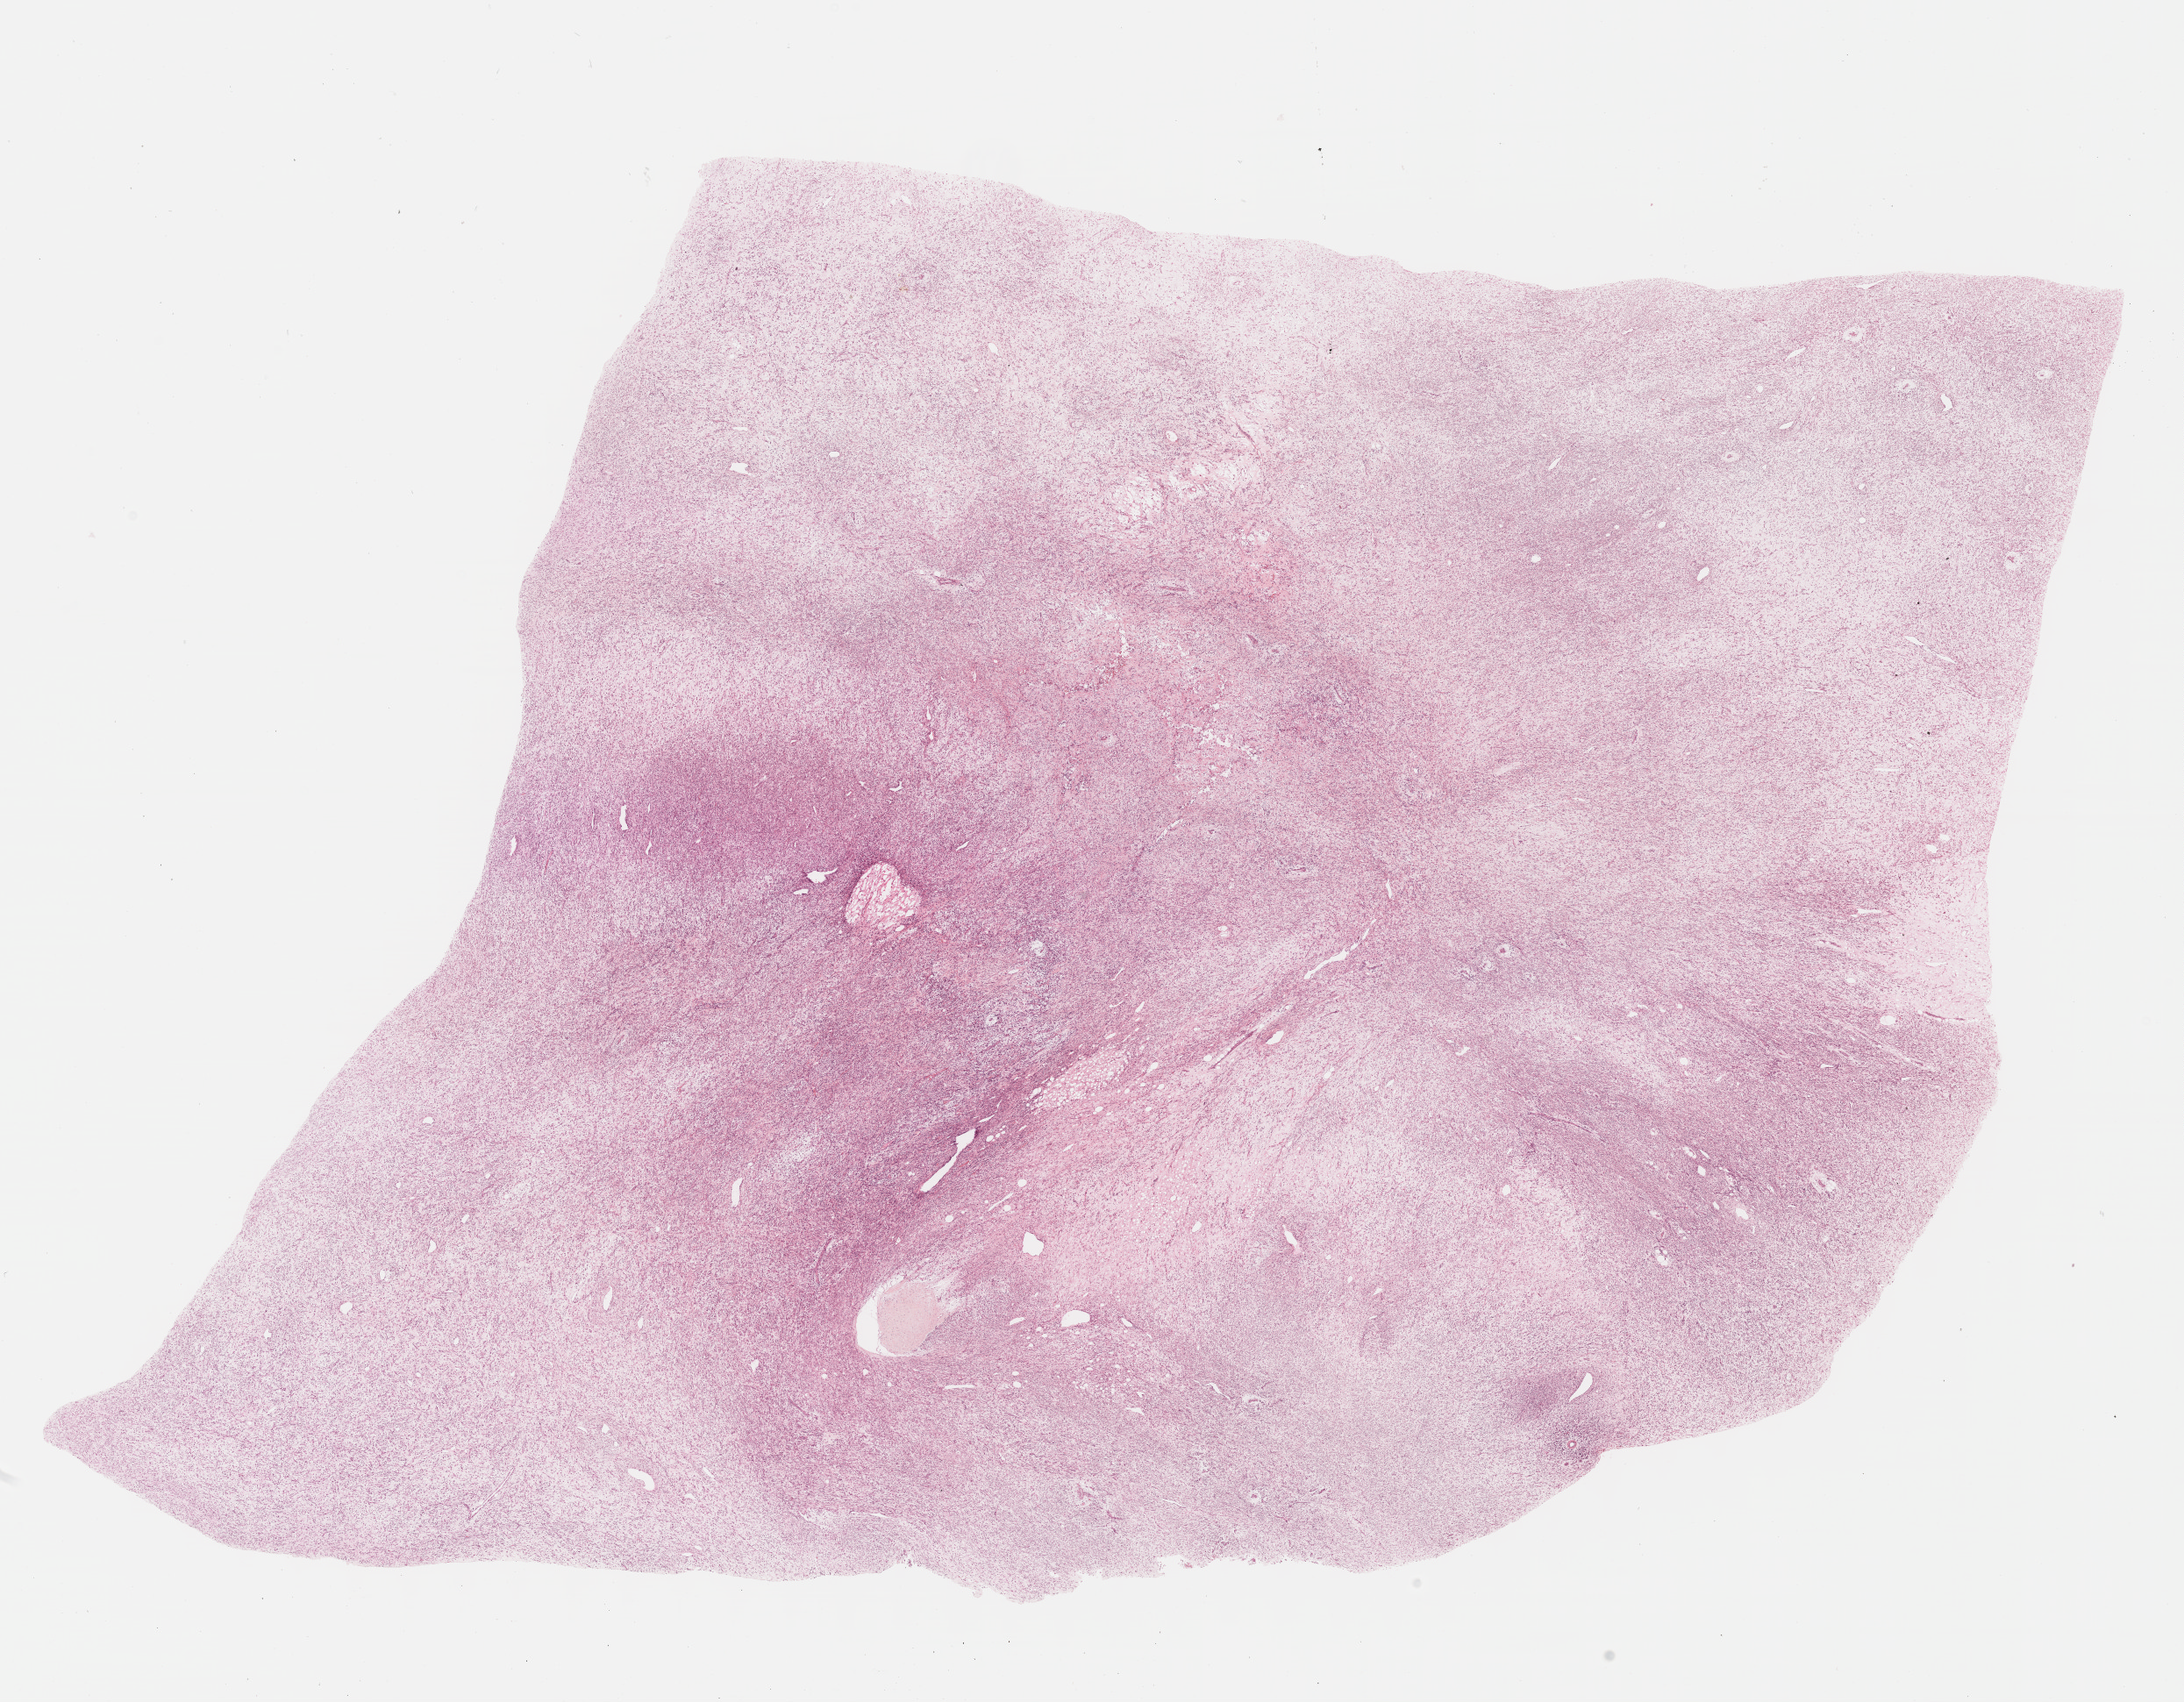
H&E whole-slide image, whole scanned area (about 20.1 x 15.7 mm, from a 40x scan) shown as a low-resolution overview, formalin-fixed paraffin-embedded (FFPE) diagnostic section, sample: primary tumour, connective, subcutaneous and other soft tissues. Male, age 37 years at initial diagnosis.
- pathologic diagnosis: Dedifferentiated liposarcoma (connective, subcutaneous and other soft tissues of lower limb and hip)